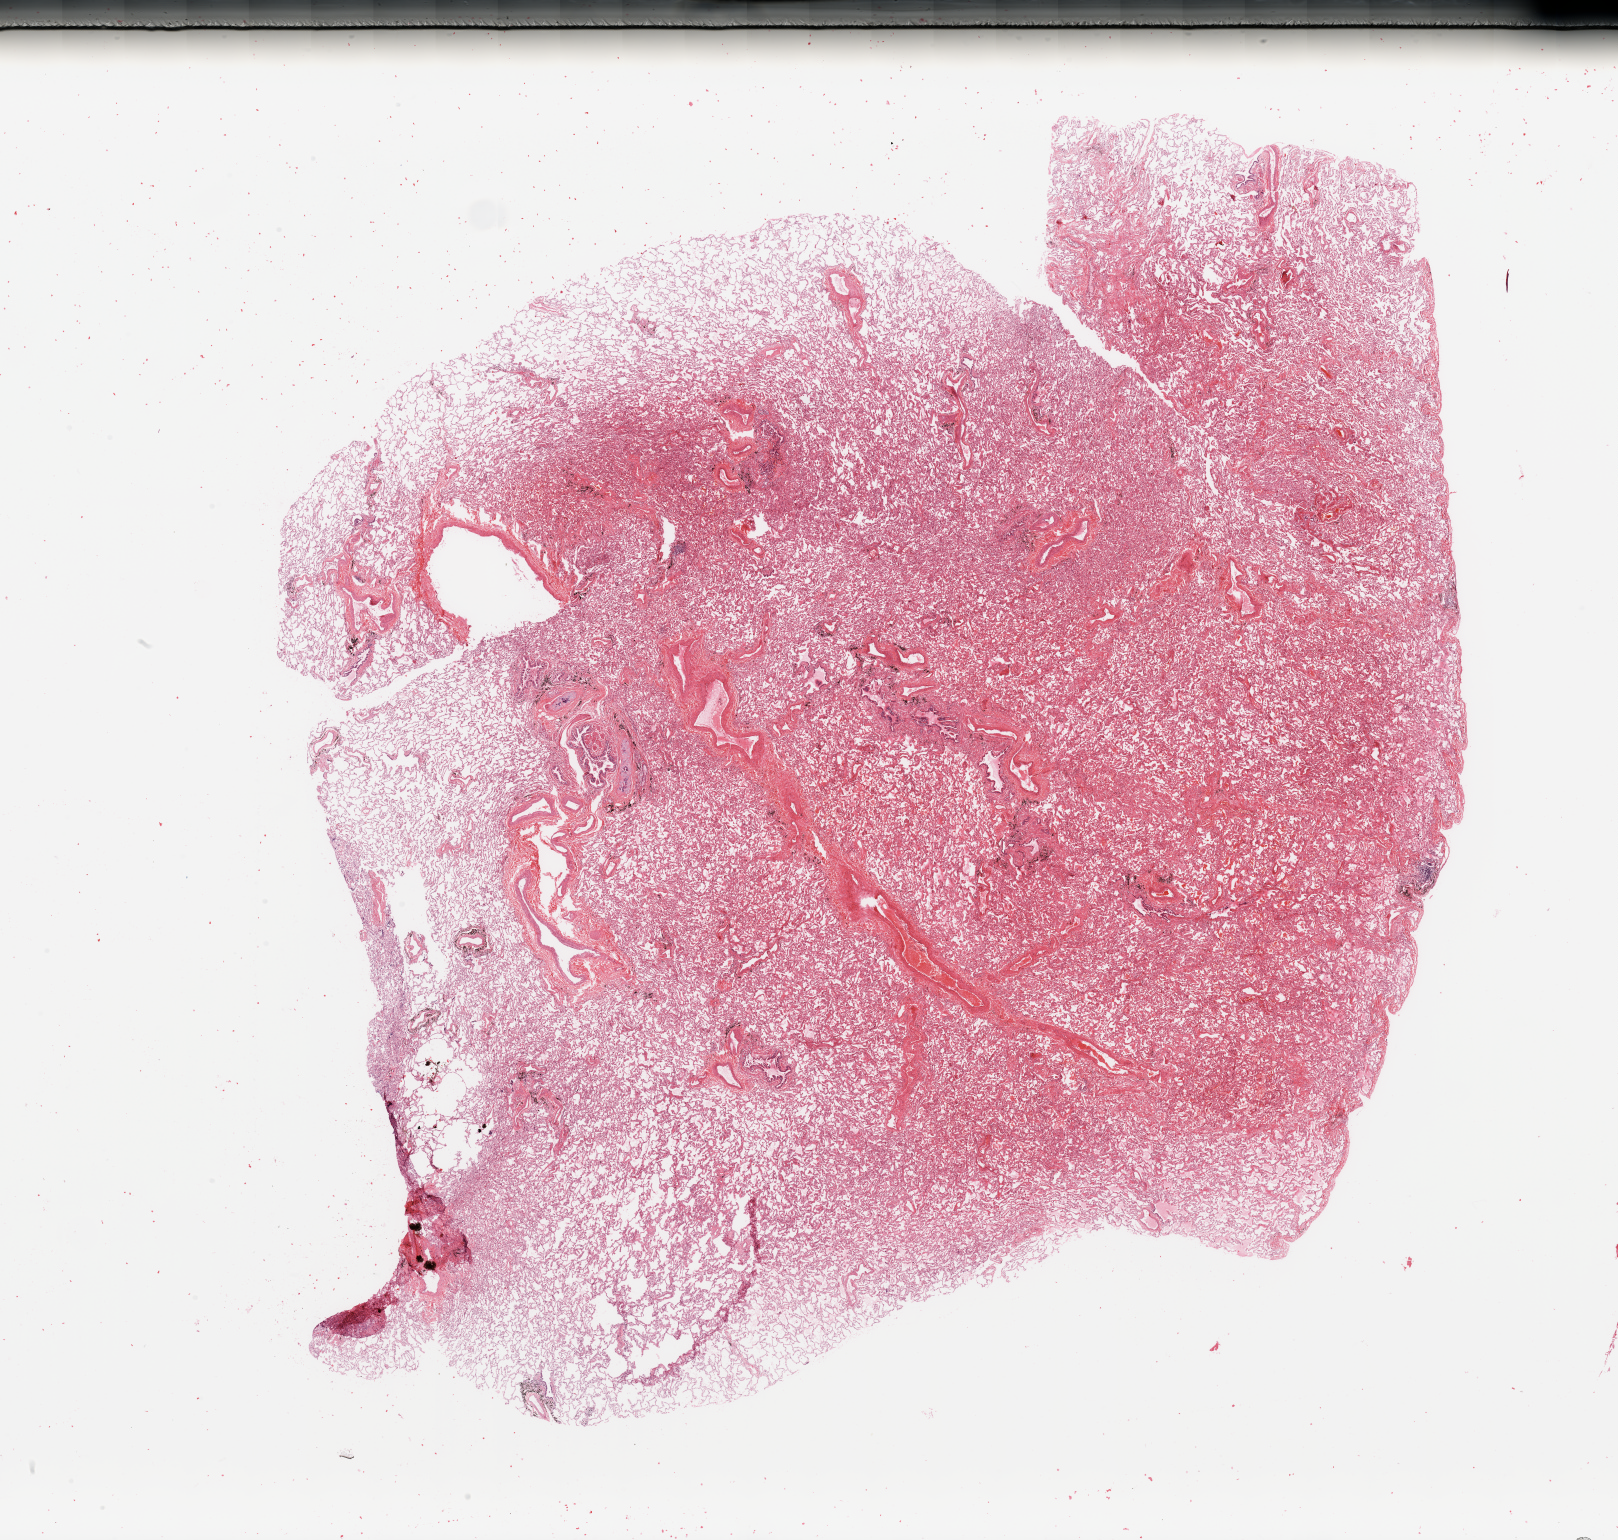
Digitized H&E-stained tissue section (whole slide) — whole scanned area (about 25.6 x 24.4 mm, from a 20x scan) shown as a low-resolution overview; lung, normal (non-tumour) tissue. Patient: female, age 54 years.
This section: normal (non-tumour) tissue from the same patient. Patient diagnosis: Adenocarcinoma, NOS.